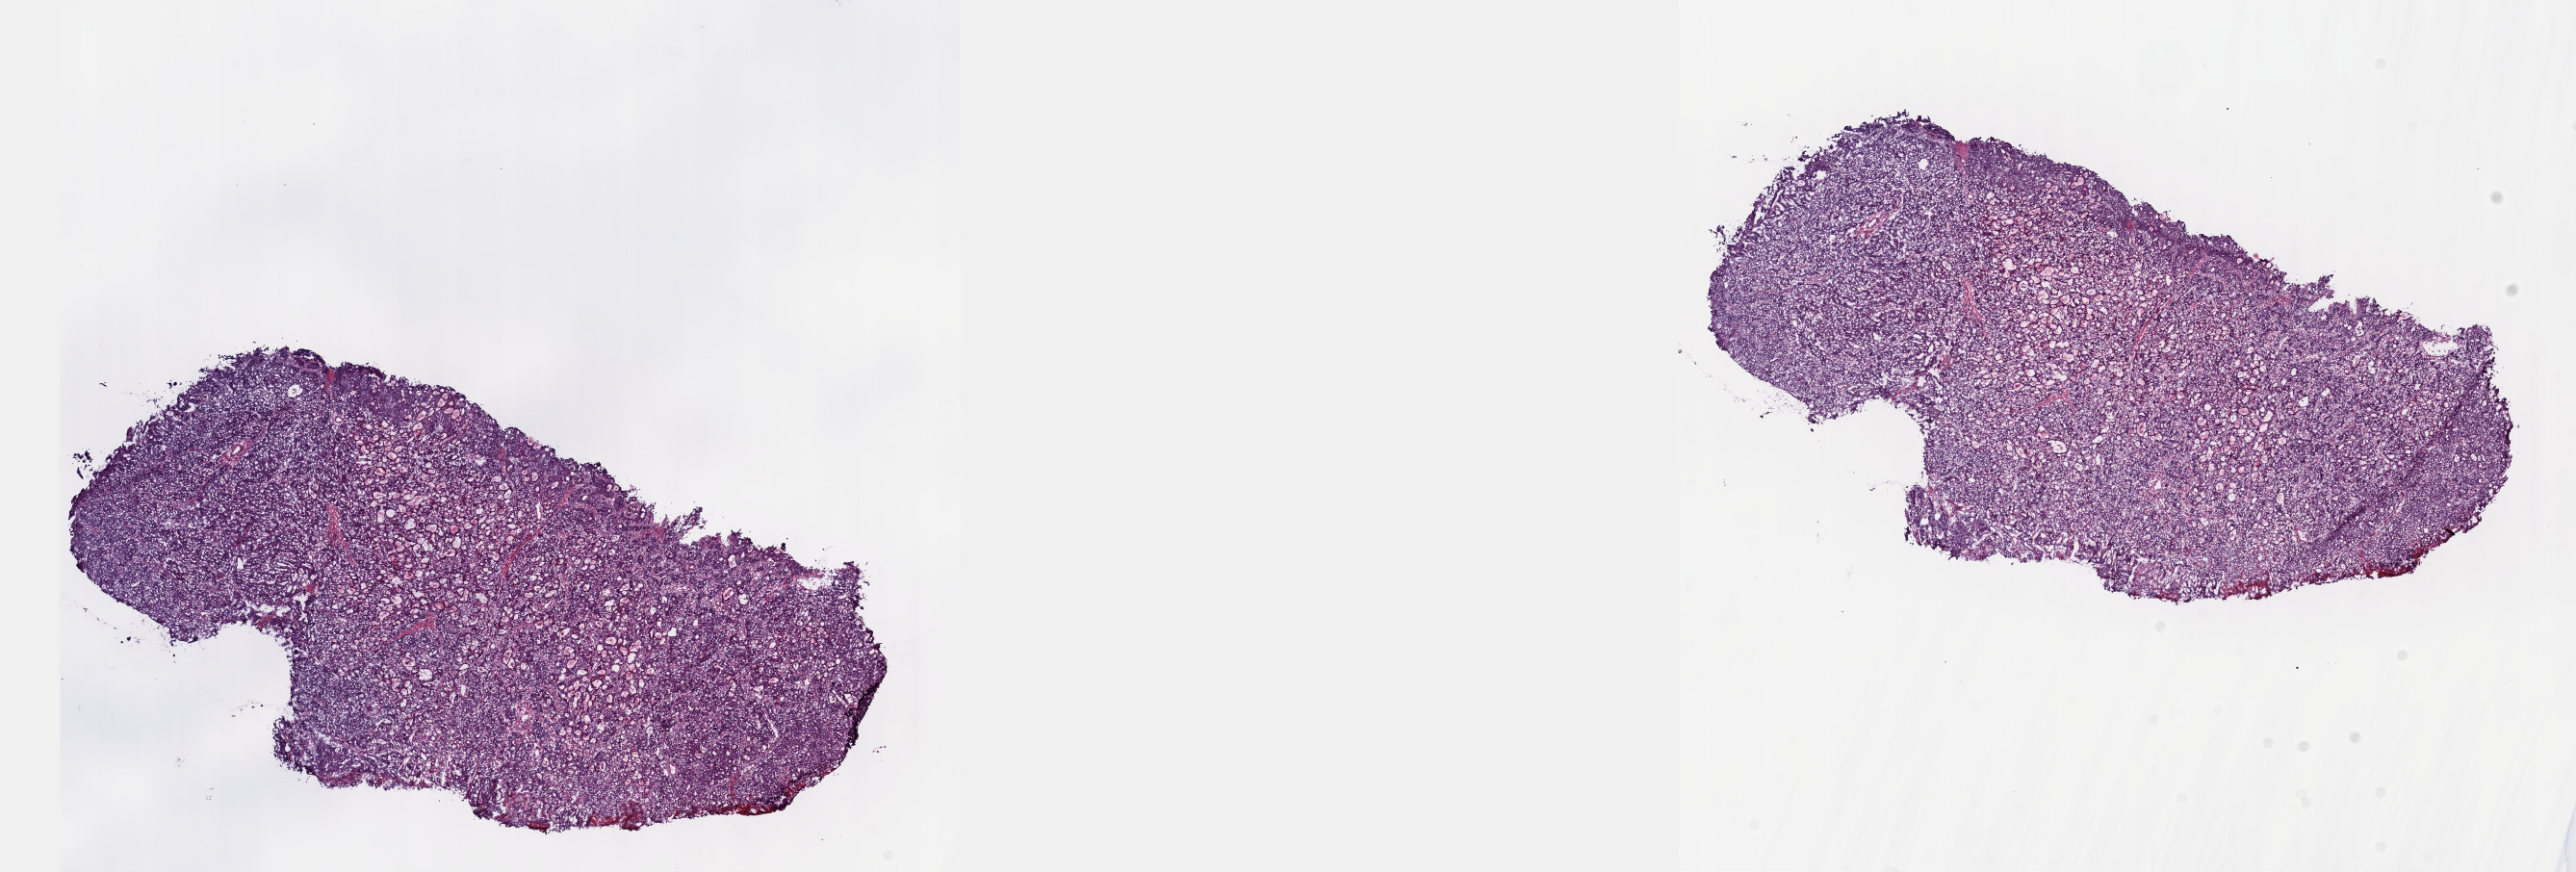
Hematoxylin and eosin (H&E) stained whole-slide image, shown as a low-resolution overview of the whole scanned area (about 21.6 x 7.3 mm). Frozen section from the top of the tissue portion. Primary tumour sample from the stomach. Male patient; age at initial diagnosis 65 years. Histologic grade: G3 (poorly differentiated). Pathologist review of this section (percent, as recorded): tumour cells 100%, tumour nuclei 75%, normal cells 0%, stromal cells 0%, necrosis 0%. Infiltration values recorded for this section: lymphocyte infiltration 5%, monocyte infiltration 0%, neutrophil infiltration 0%.
AJCC pathologic stage: IIIB (7th edition). TNM: T4b N0 M0. Pathologic diagnosis: Adenocarcinoma, intestinal type (body of stomach).